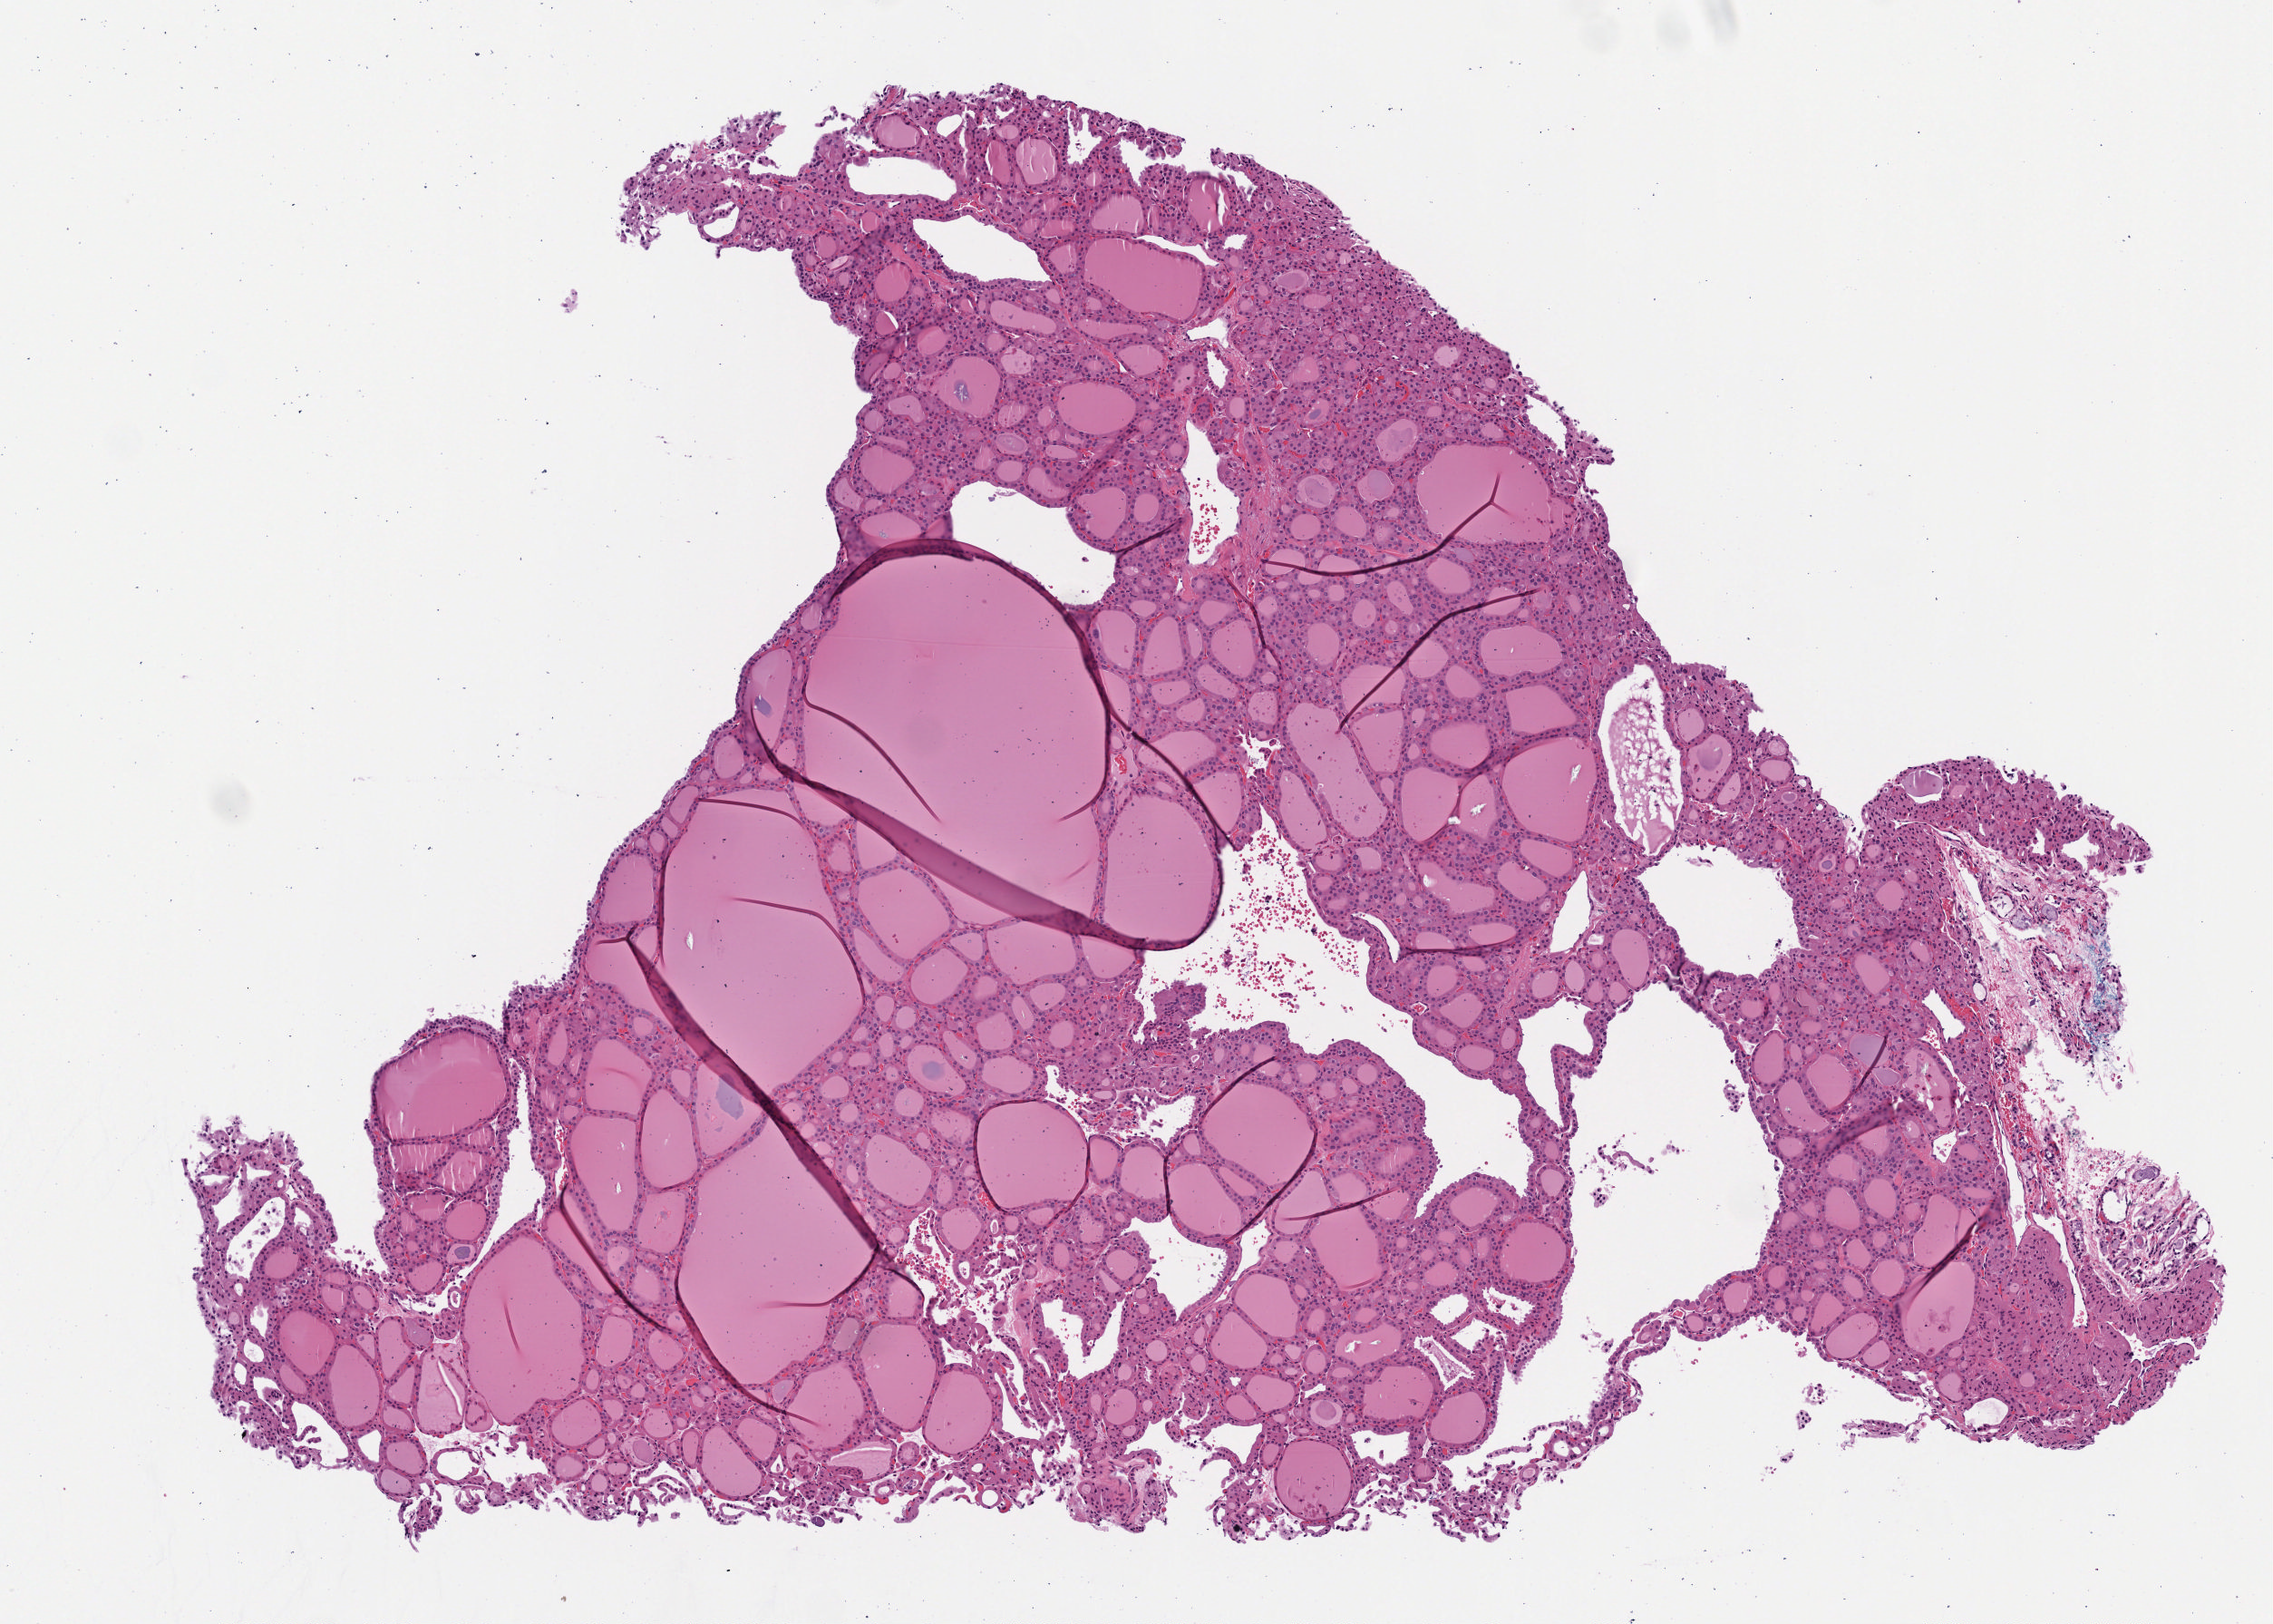
Hematoxylin and eosin (H&E) stained whole-slide image, a low-resolution overview of the entire scanned area, about 5.1 x 3.6 mm (from a 40x scan), formalin-fixed paraffin-embedded (FFPE) diagnostic section, sample: primary tumour, thyroid. Patient: female, age at initial diagnosis 66 years.
Histologic diagnosis: Papillary carcinoma, follicular variant.